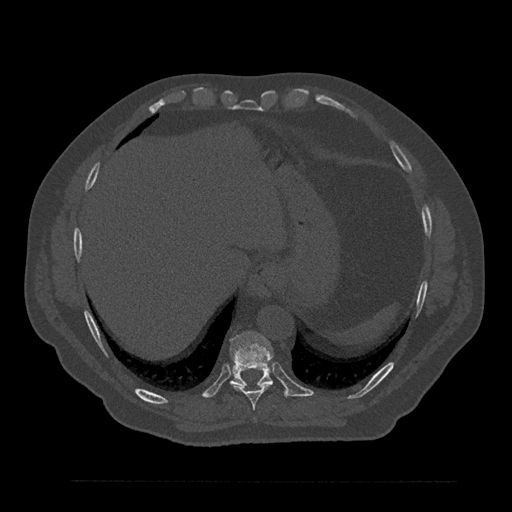
CT including the spine, one axial slice. Position 380 of 797 along the scan axis. Reconstruction kernel Br40s/3. 120 kVp. Bone window (W 1800 / L 400 HU). 0.5 mm slice thickness. 512 × 512 image matrix, field of view 430 × 430 mm. Patient: male, 61 years. From the clinical record (not read from this slice): primary cancer: prostate.
Structures marked on this image (semi-automatic segmentation, software-assisted and operator-edited):
- T10 vertebra: bounding box <229,331,273,386> (left, top, right, bottom; pixels)
- T9 vertebra: <231,383,273,410>